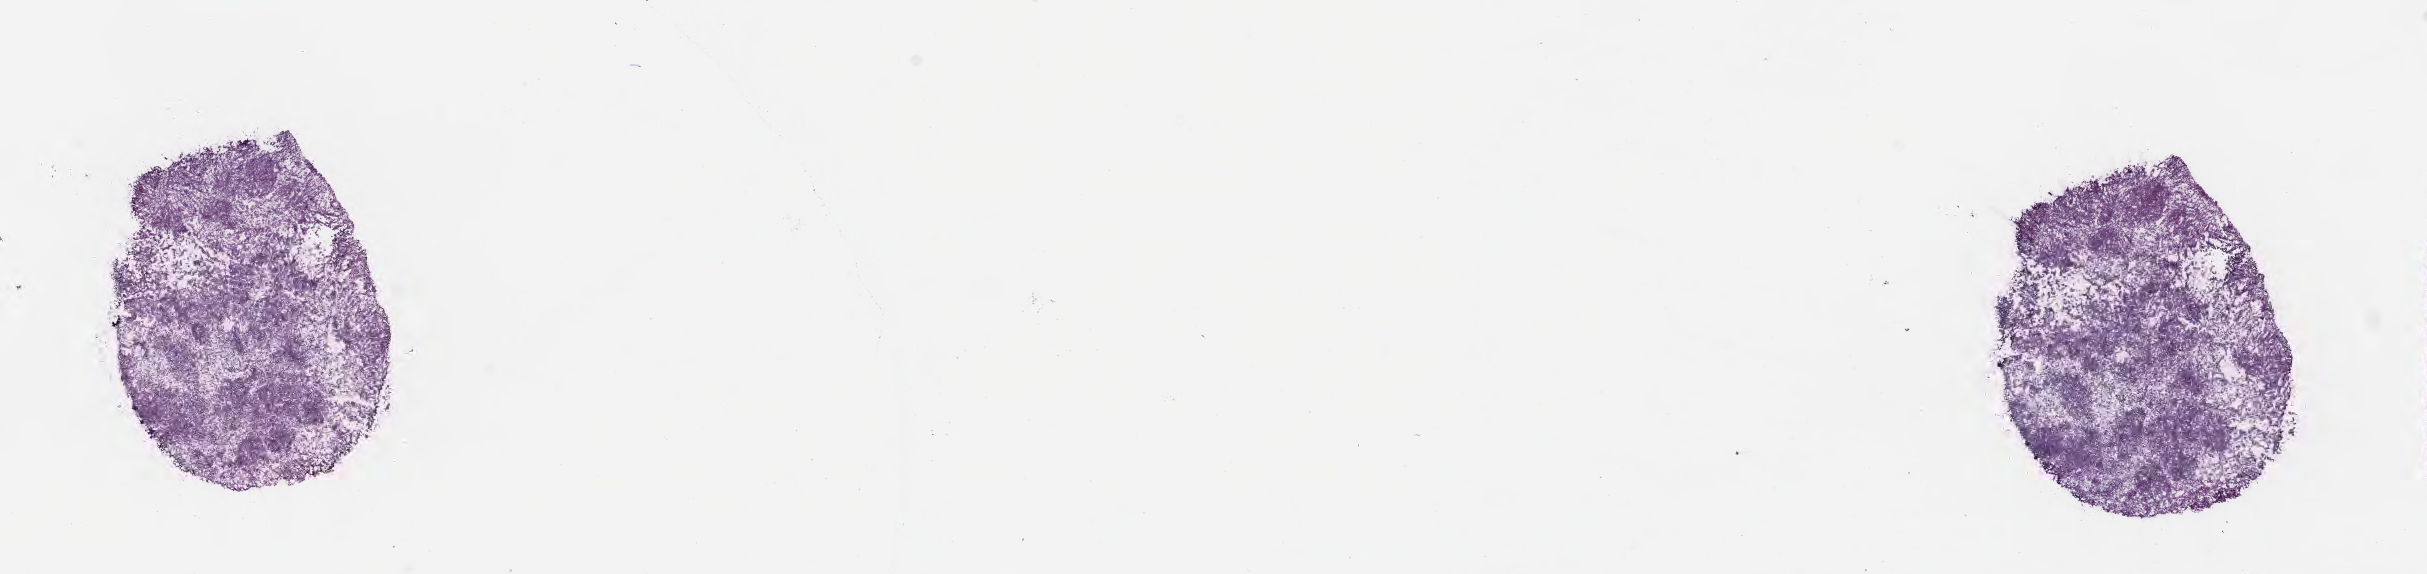
Whole-slide image, H&E stain — whole scanned area (about 19.6 x 4.6 mm) shown as a low-resolution overview. Cryosection. Primary tumor. Anatomic site: kidney (left). Patient: male, age at initial diagnosis 0 years. Composition of this section per pathologist review: tumor cells 90%, tumor nuclei 90%, stromal cells 9%, necrosis 1%, normal cells 0%. Infiltration values recorded for this section: lymphocyte infiltration 2%, monocyte infiltration 1%, neutrophil infiltration 3%.
Section: top of the tissue portion. Histologic diagnosis: Nephroblastoma, NOS.